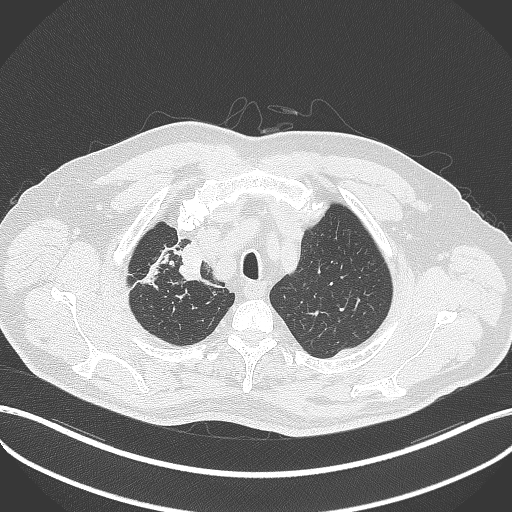
Chest CT, one axial slice; position 329 of 411 along the scan axis; lung window (W 1500 / L -600 HU); 1 mm slice thickness; 512 × 512 image matrix, field of view 400 × 400 mm. Patient: male, 60 years. Case-level facts recorded for this patient, not image findings: clinical TNM (as recorded): T1b N1 M0.
Structures marked on this image (rectangle marked by the reading radiologist):
- lung tumour (recorded histology: squamous cell carcinoma): box from (x=176, y=242) to (x=223, y=294) px